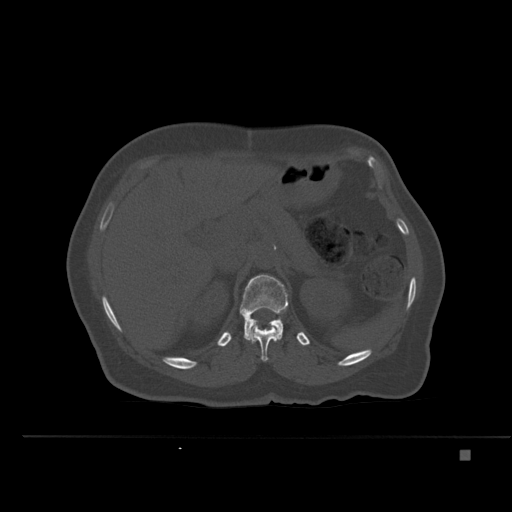
CT including the spine, one axial slice. Slice 245 of 477 in the series (ordered by position). Bone window (W 1800 / L 400 HU). 1.5 mm slice thickness. 512 × 512 image matrix, field of view 422 × 422 mm. Female patient, age 74 years. From the clinical record (not read from this slice): primary cancer: colon.
Annotated regions visible in this slice (semi-automatic segmentation, software-assisted and operator-edited):
- L1 vertebra: box from (x=240, y=274) to (x=288, y=341) px
- T12 vertebra: (x=250, y=310)–(x=282, y=361)